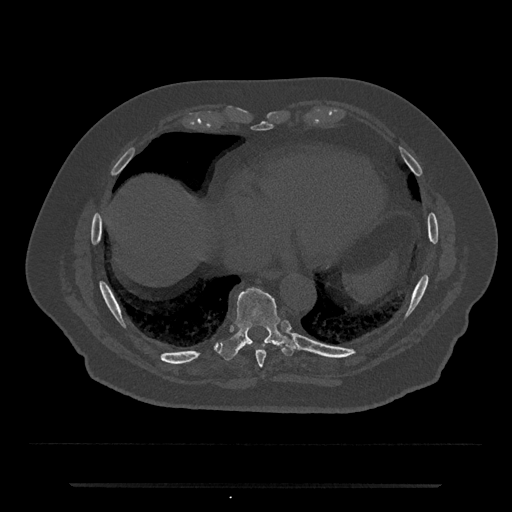
CT including the spine, one axial slice. Reconstruction kernel Br40s/3. Bone window (W 1800 / L 400 HU). 0.5 mm slice thickness. 512 × 512 image matrix, field of view 434 × 434 mm. Patient: male, 80 years. From the clinical record (not read from this slice): primary cancer: prostate.
Structures marked on this image (semi-automatic segmentation, software-assisted and operator-edited):
- T8 vertebra: bounding box [x1, y1, x2, y2] px = [256, 350, 266, 368]
- T9 vertebra: [217, 287, 299, 361]